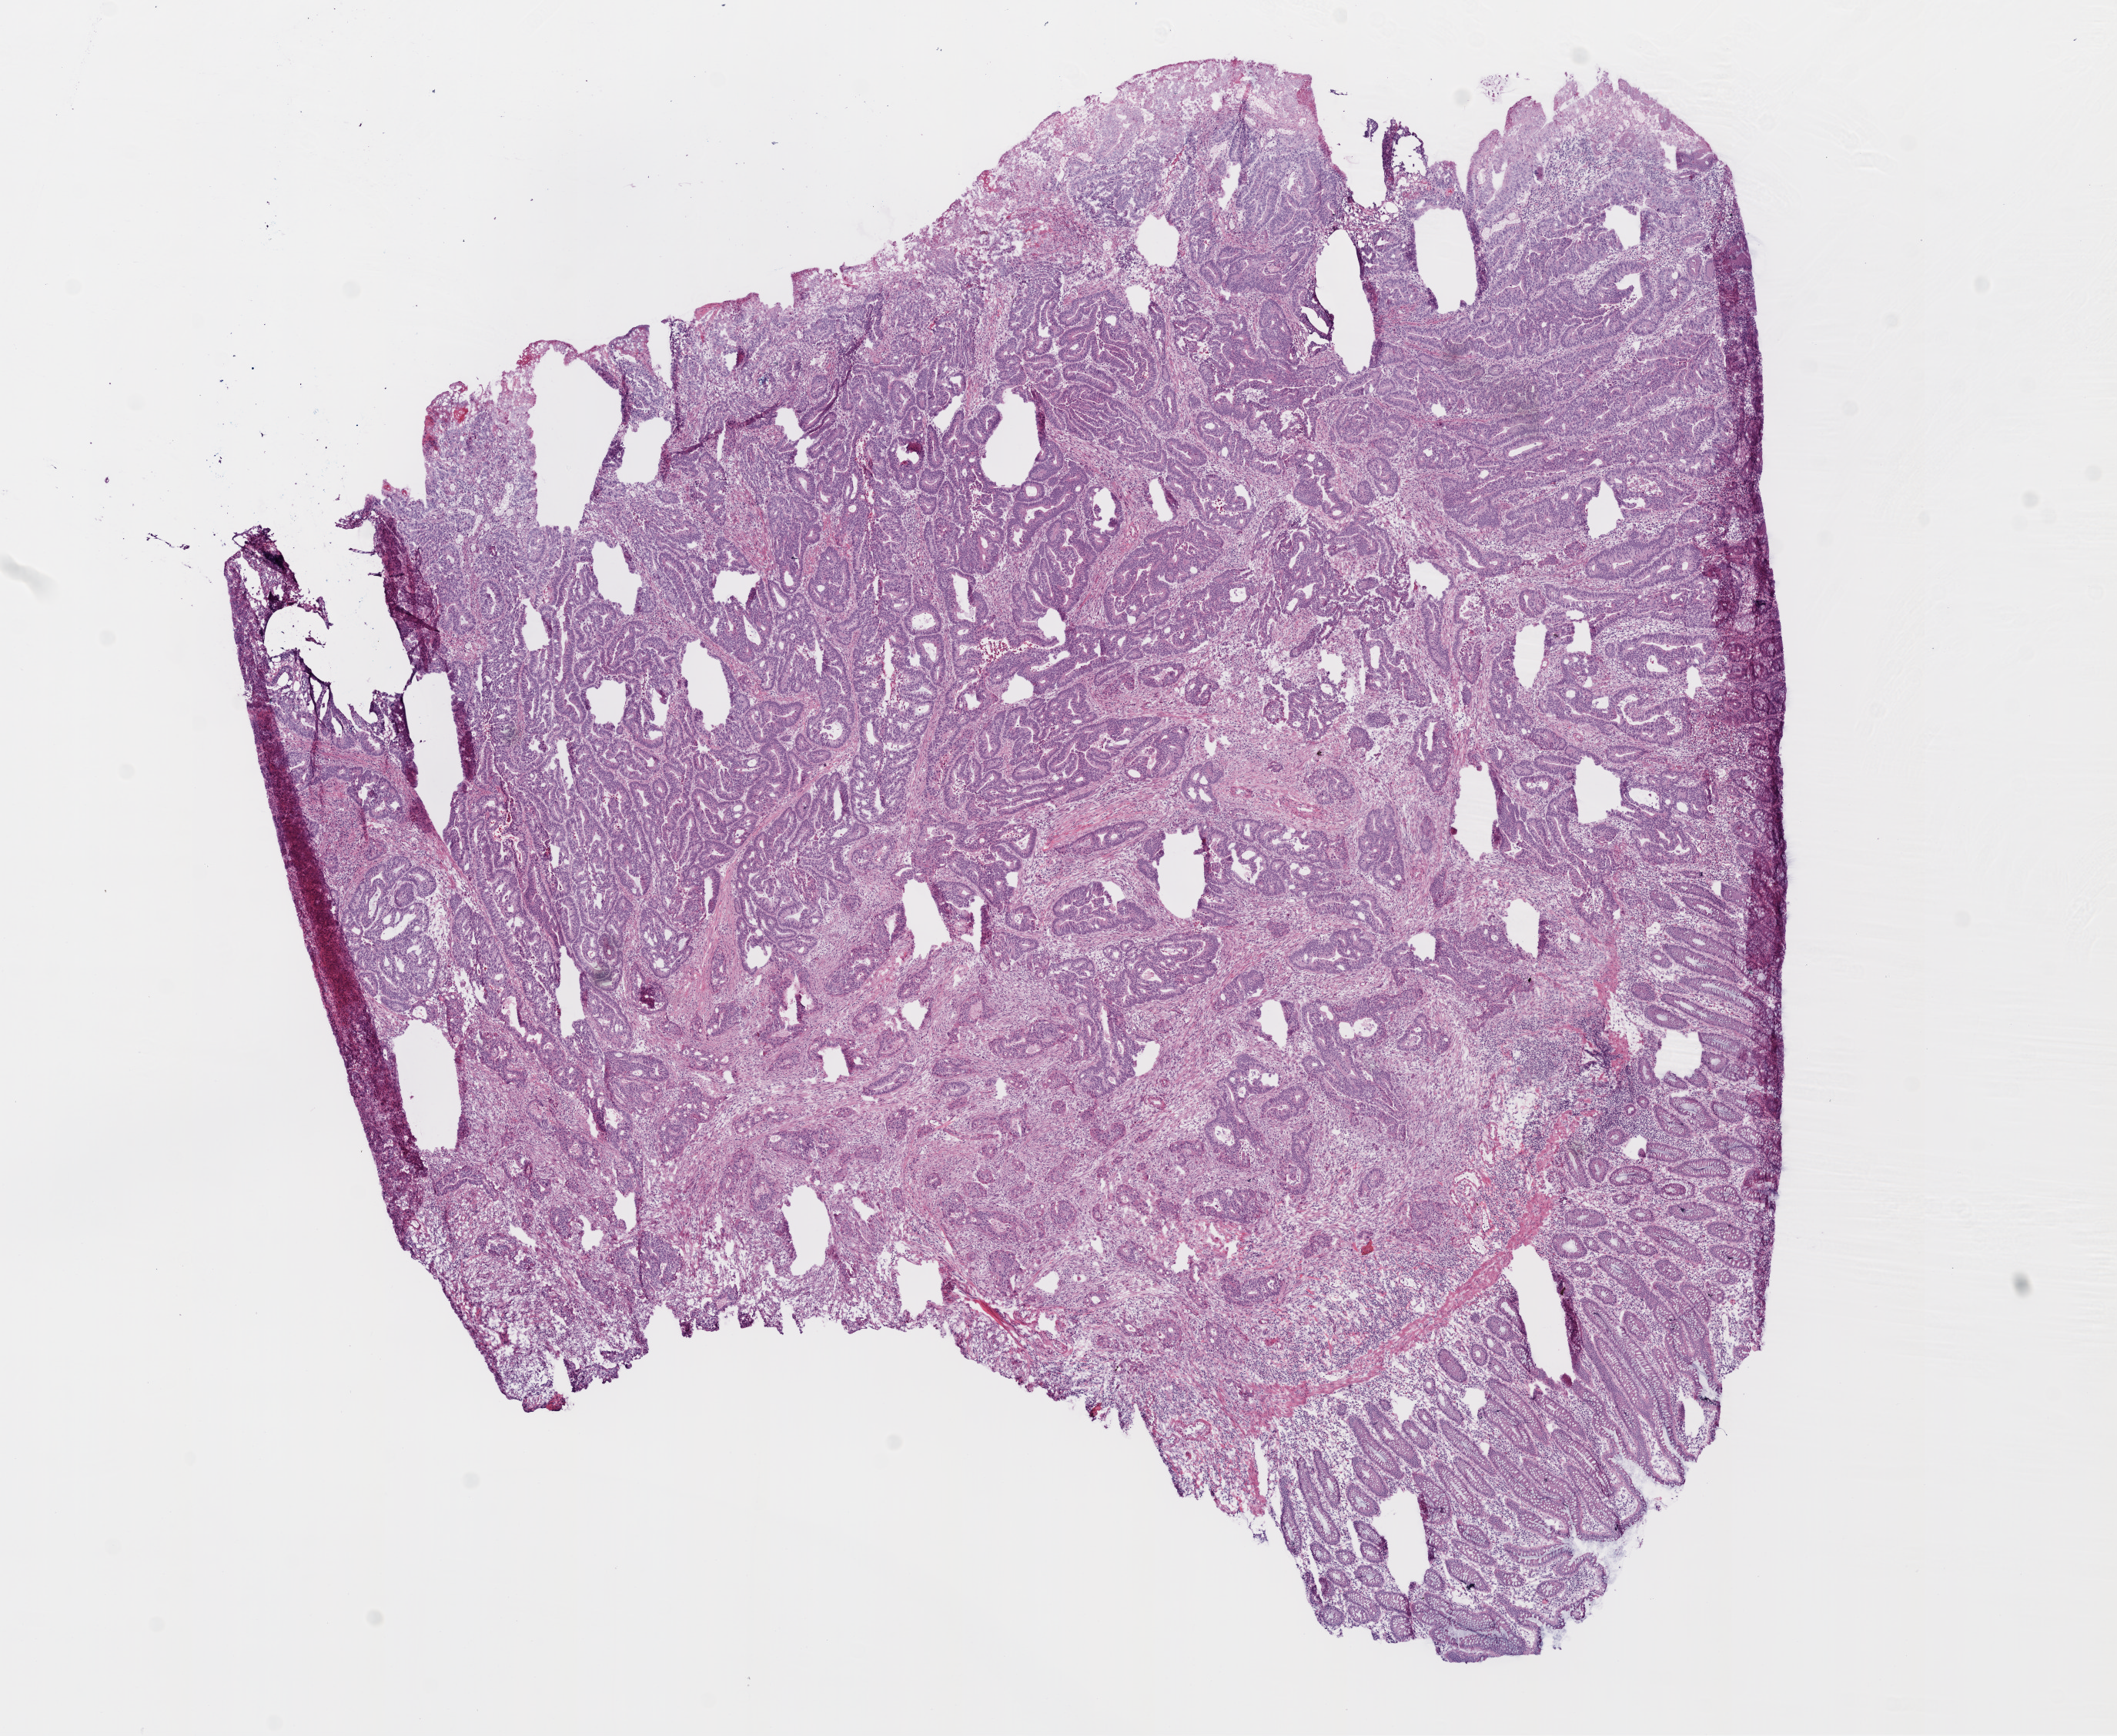
Hematoxylin and eosin (H&E) stained whole-slide image — a low-resolution overview of the entire scanned area, about 11.0 x 9.0 mm (slide scanned at 20x); frozen section from the bottom of the tissue portion; sample: primary tumour, colon. Patient: female, age at initial diagnosis 85 years. Pathologist review of this section (percent, as recorded): tumour cells 67%, tumour nuclei 75%.
Pathologic diagnosis: Adenocarcinoma with mixed subtypes.